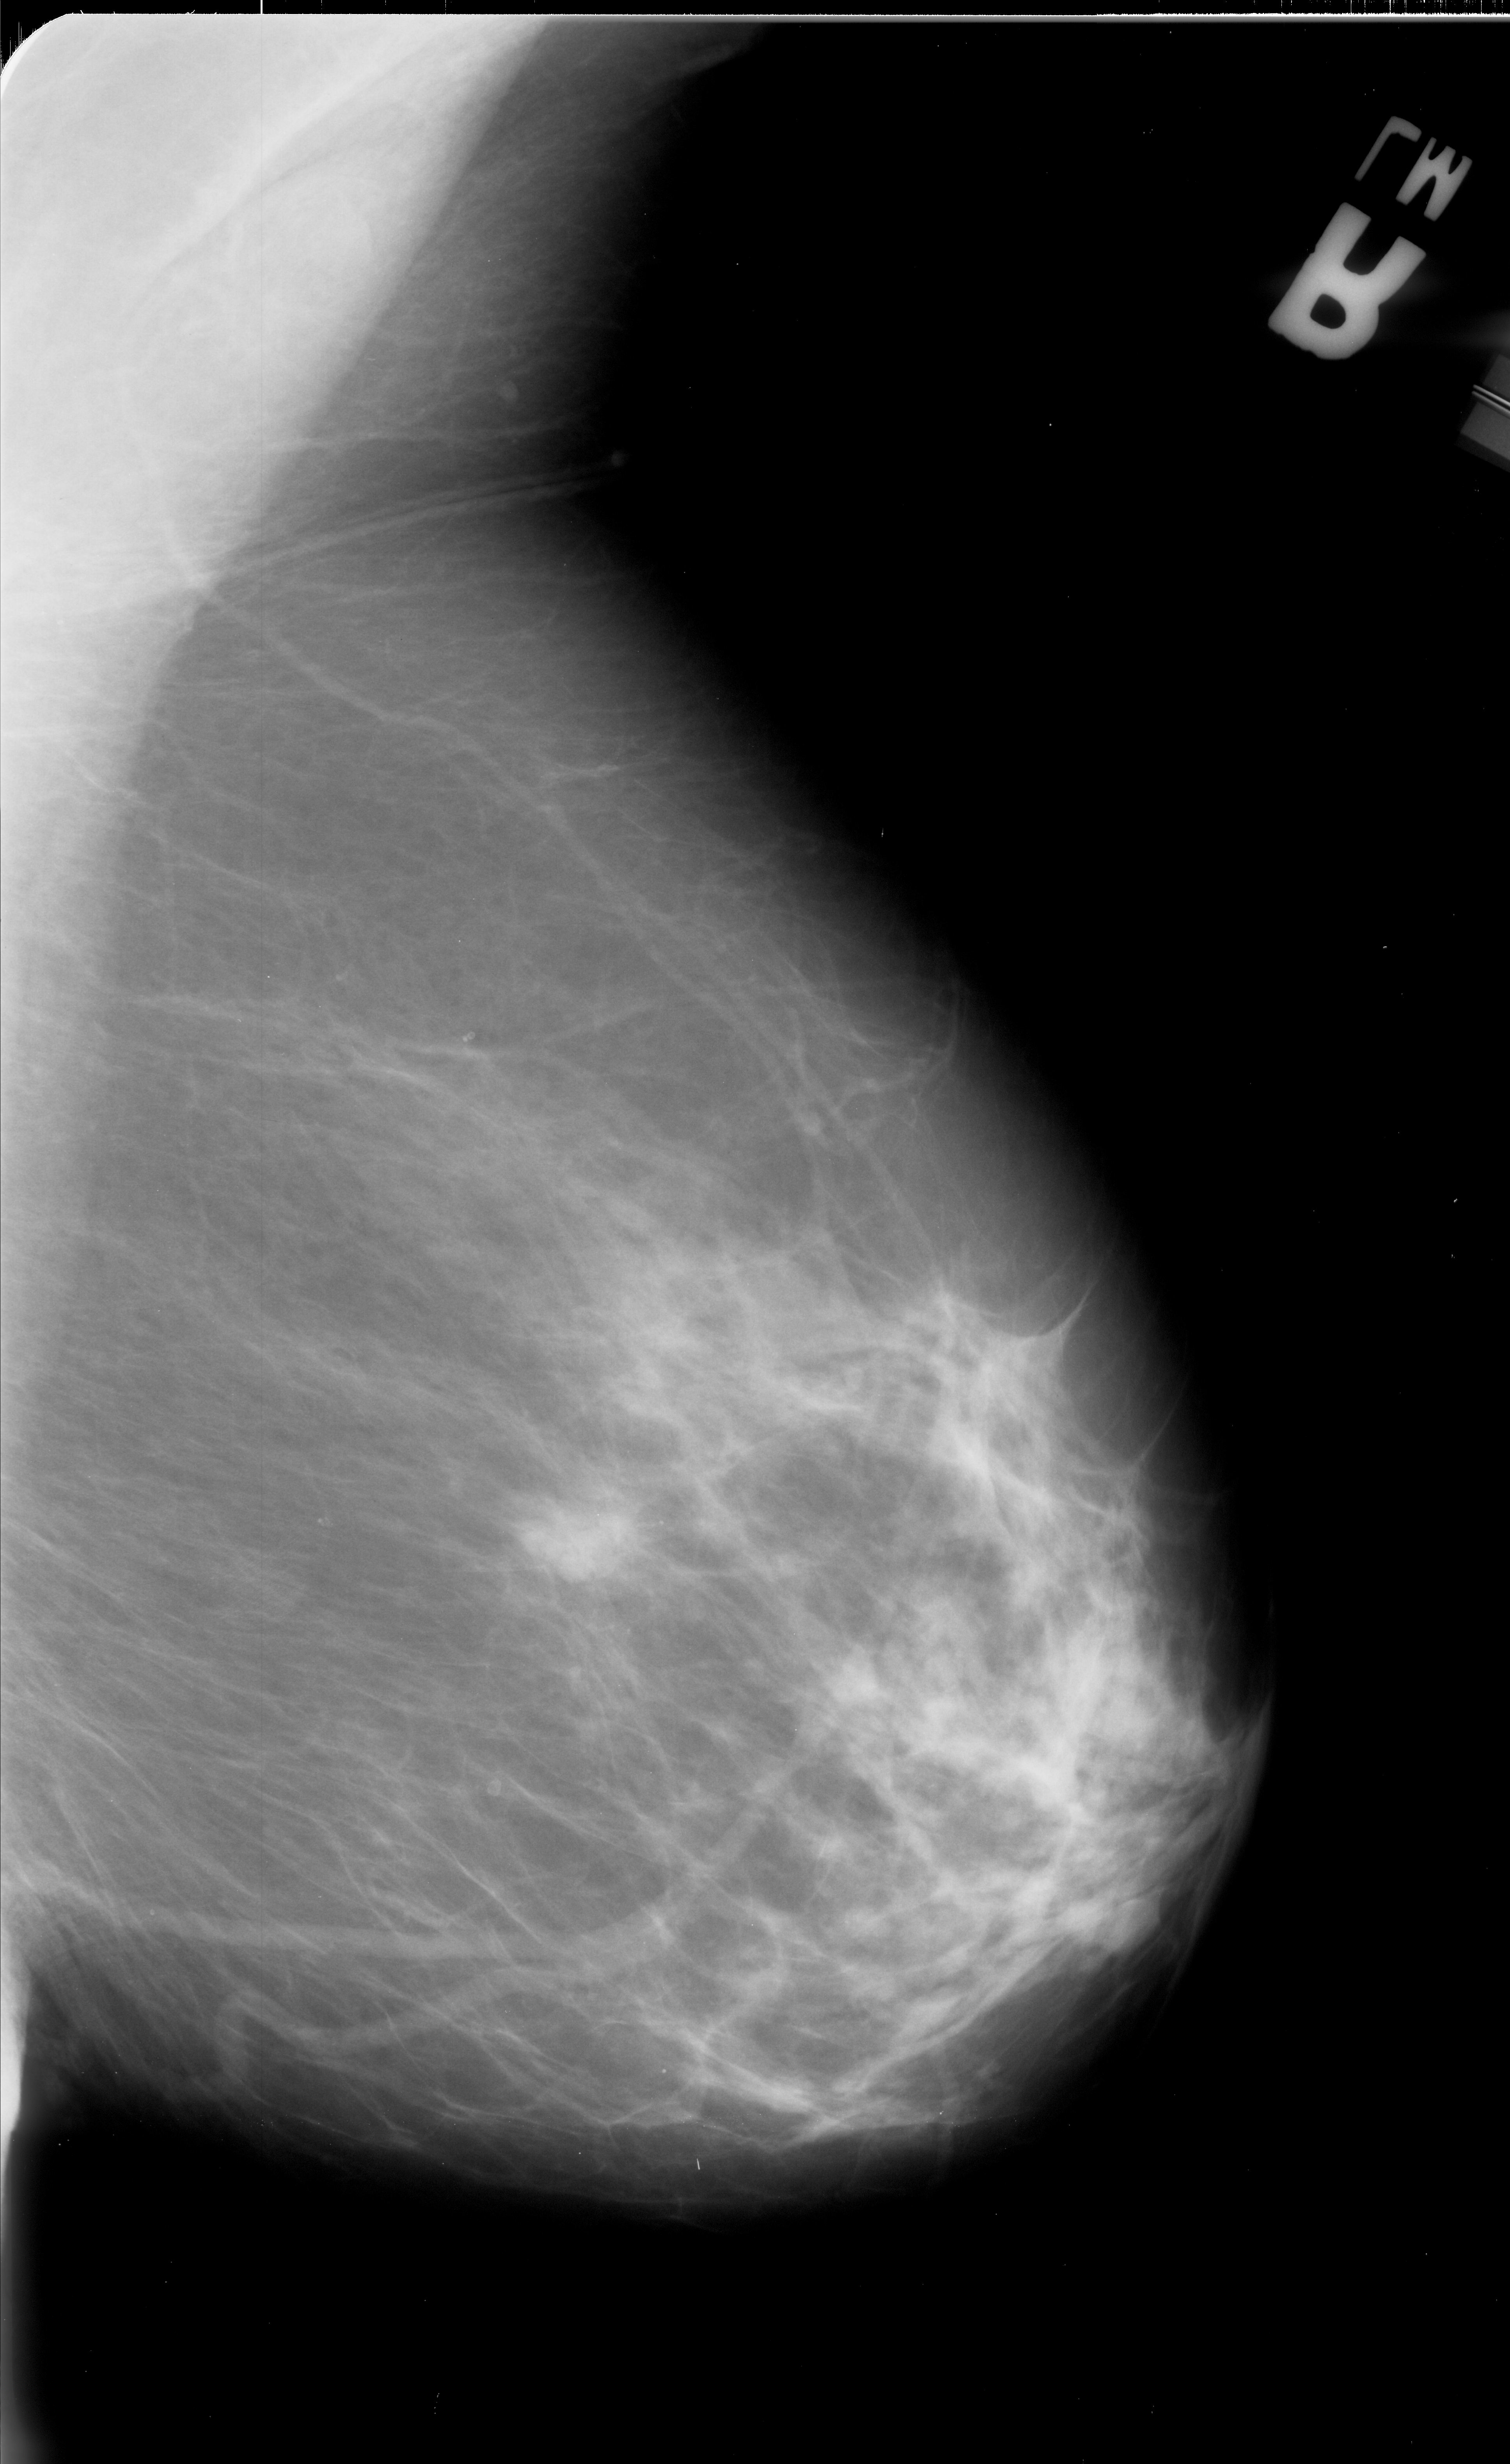
Digitized screen-film mammogram, right breast, mediolateral oblique (MLO) view.
Finding: mass, shape lobulated, margins spiculated; BI-RADS assessment category 5; pathology result (as recorded, not read from the image): malignant.